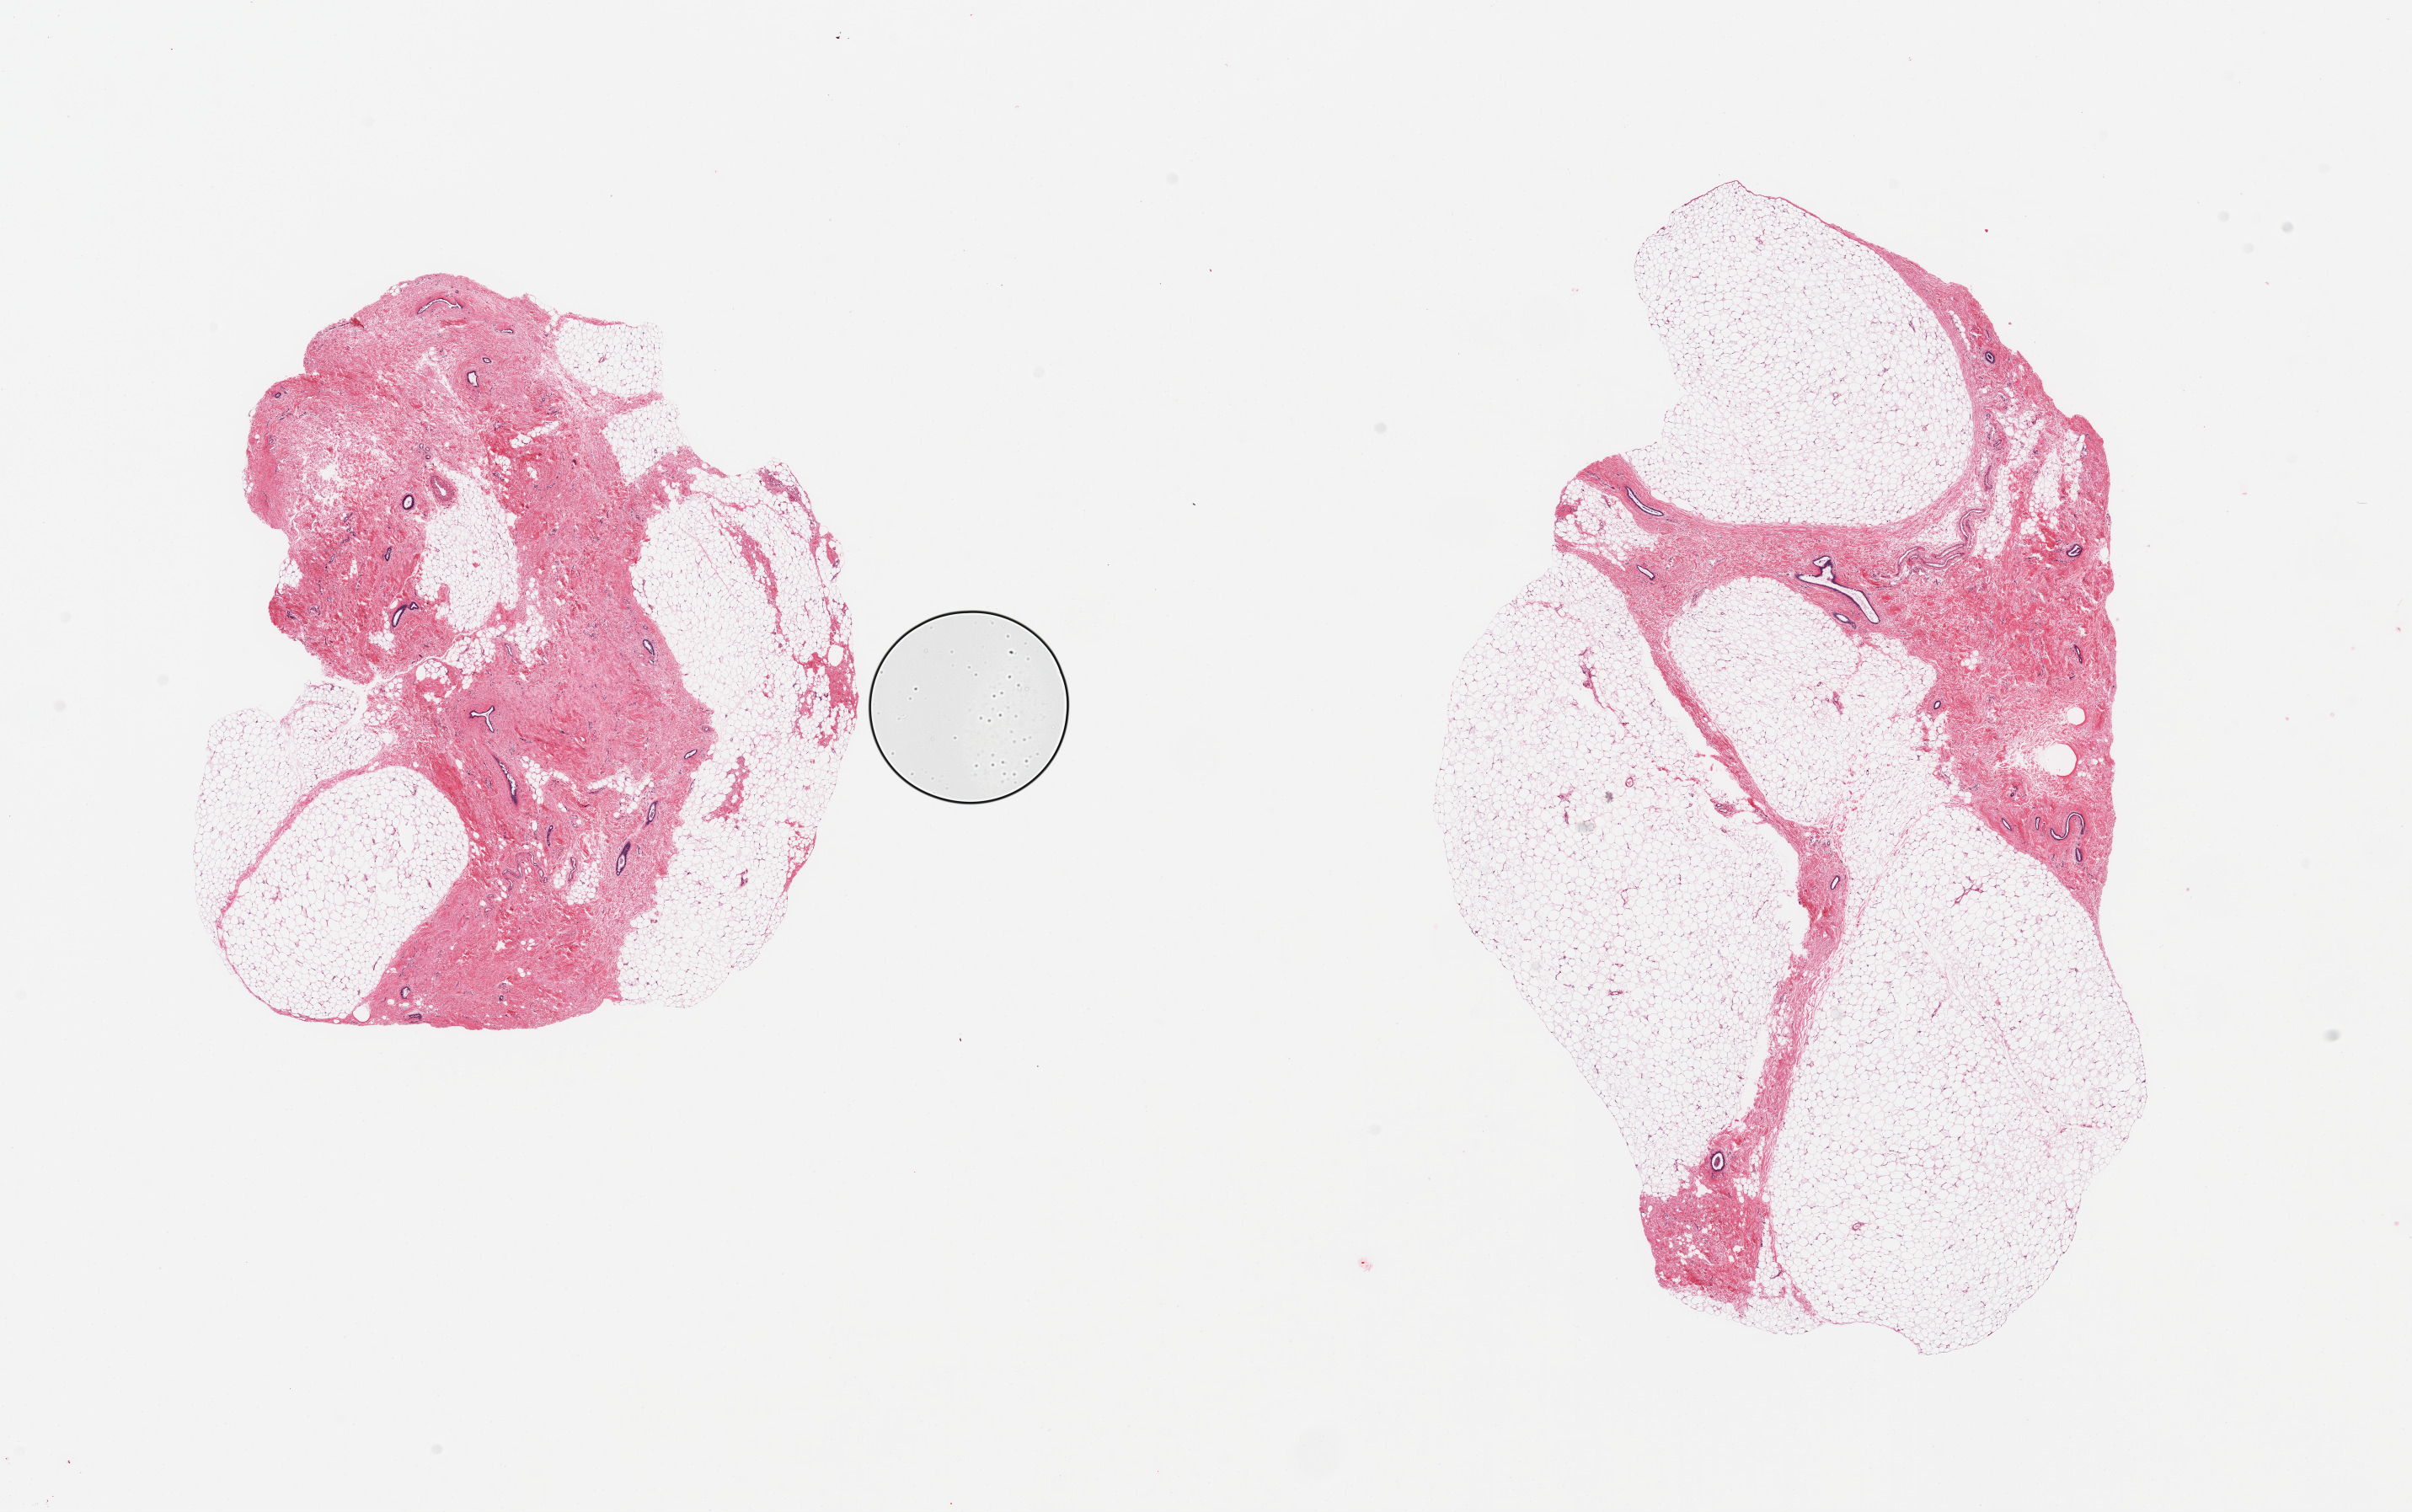
Whole-slide image, haematoxylin and eosin stain, a low-resolution overview of the entire scanned area, about 22.6 x 14.2 mm (slide scanned at 20x); PAXgene-fixed, paraffin-embedded tissue; section of breast (target tissue); donor tissue sample. Donor: male.
Review note (as recorded): 2 pieces, moderate gynecomastoid stromal and ductal hyperplasia.